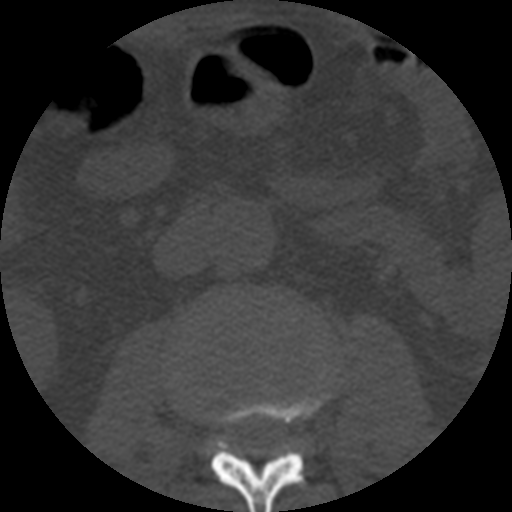
CT including the spine, one axial slice. Bone window (W 1800 / L 400 HU). 1.25 mm slice thickness. 512 × 512 image matrix. Patient age 57 years. From the clinical record (not read from this slice): primary cancer: prostate.
Structures marked on this image (semi-automatically segmented with operator editing):
- L2 vertebra: bounding box (x1, y1, x2, y2) in pixels: (207, 386, 330, 512)